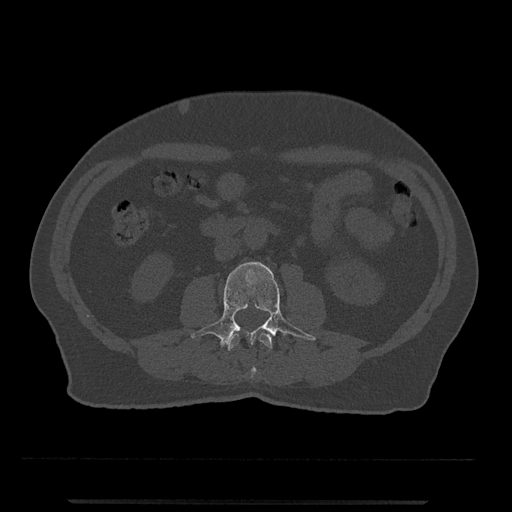
CT including the spine, one axial slice; slice 211 of 797 in the series (ordered by position); 120 kVp; bone window (W 1800 / L 400 HU); 0.5 mm slice thickness; 512 × 512 image matrix, field of view 419 × 419 mm. Patient: male, 63 years. Case-level facts recorded for this patient, not image findings: primary cancer: prostate.
Outlined on this slice (semi-automatically segmented with operator editing):
- L2 vertebra: bounding box (x1, y1, x2, y2) in pixels: (227, 332, 272, 379)
- L3 vertebra: (191, 262, 316, 348)